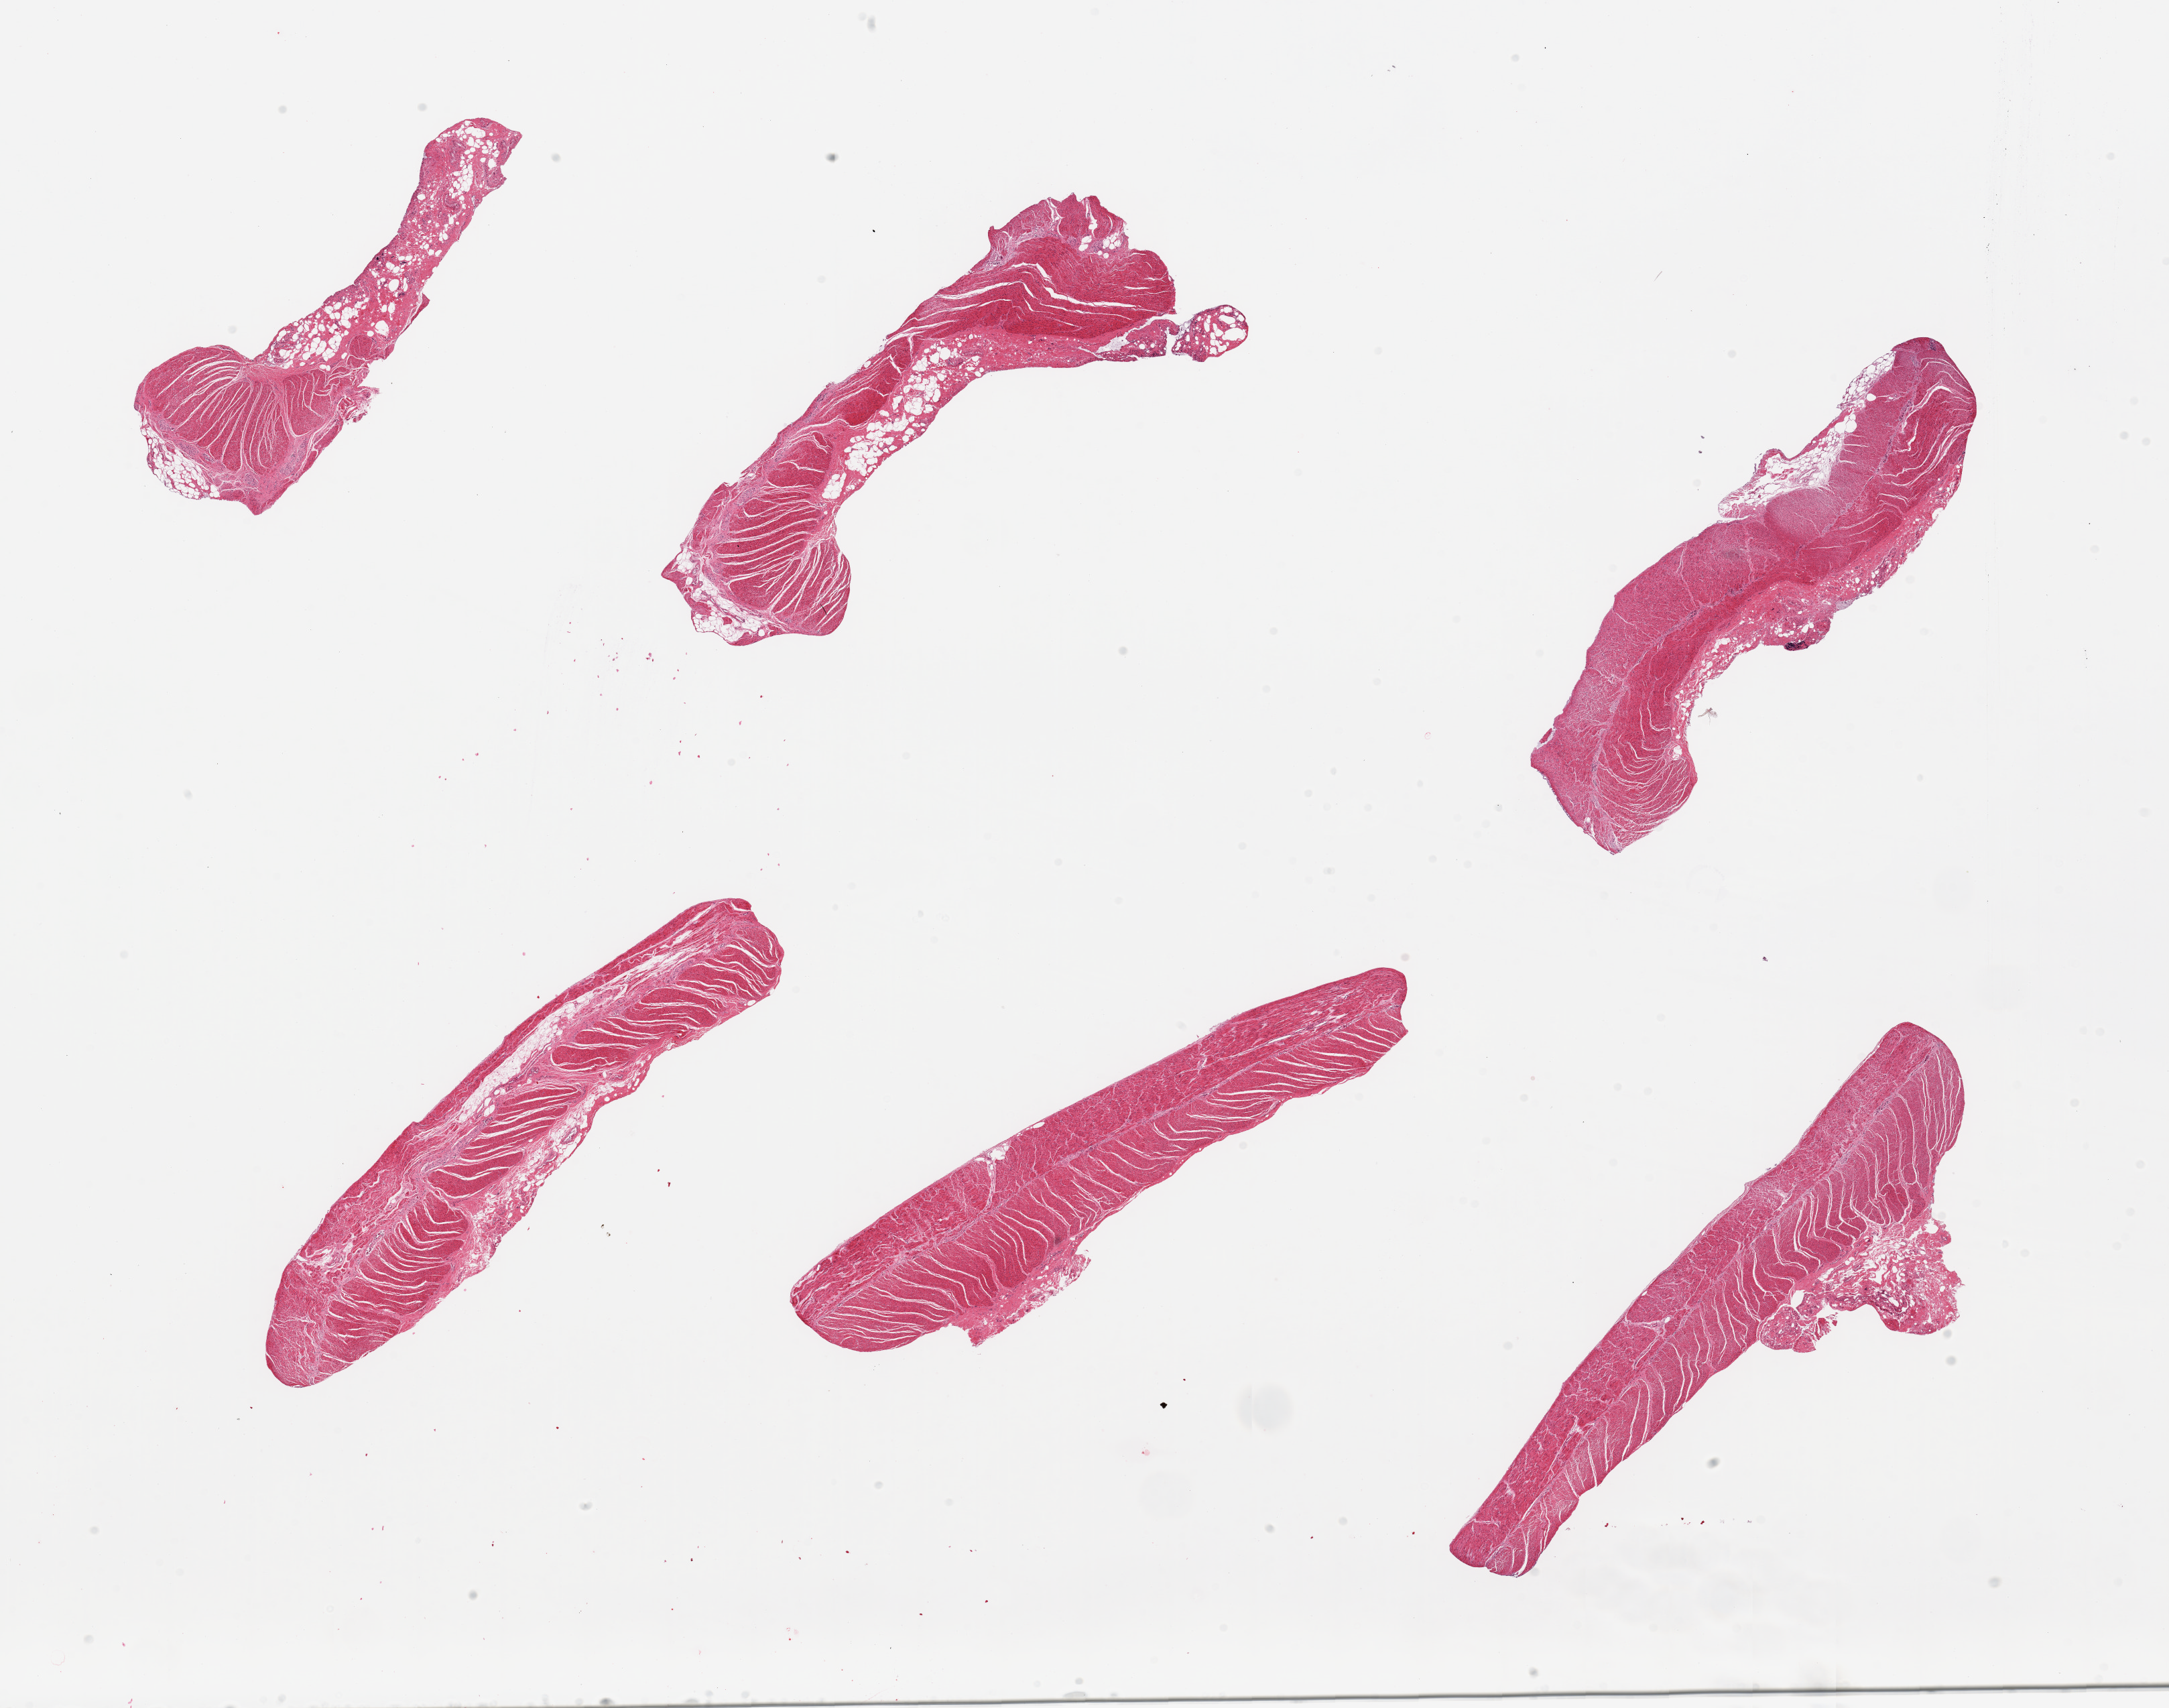
Hematoxylin and eosin (H&E) whole-slide image, shown as a low-resolution overview of the whole scanned area (about 25.6 x 20.2 mm, from a 20x scan), PAXgene-fixed paraffin-embedded (PFPE) section, section of sigmoid colon (target tissue), donor tissue sample. Donor sex: female.
* pathologist's review note for this sample: 6 pieces; muscularis with some attached submucosa/fat